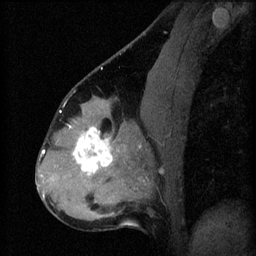
Breast MRI (dynamic contrast-enhanced), one sagittal slice; slice 30 of 60 in the series (ordered by position); 3 images stored at this slice position (order not interpretable as contrast timing); 1.5 T; TE 4.2 ms, TR 8.2 ms; 2.3 mm slice thickness; 256 × 256 image matrix, field of view 180 × 180 mm. Patient: female, 37 years.
Annotated regions visible in this slice (semi-automatic segmentation, software-assisted and operator-edited):
- analysis volume of interest (the breast-tissue region the enhancement analysis was run in; not a lesion): box from (x=67, y=120) to (x=122, y=179) px
- tumour enhancement mask (voxels above the 70 % enhancement threshold inside the analysis volume of interest): (x=69, y=126)–(x=113, y=175)